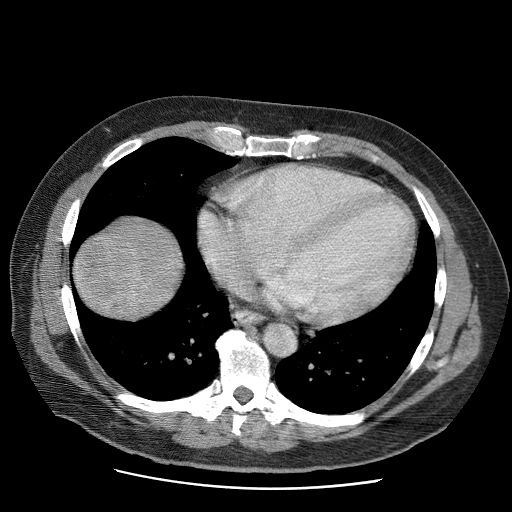
Contrast-enhanced abdominal CT (liver protocol), one axial slice. Position 65 of 81 along the scan axis. Reconstruction kernel STANDARD. Soft-tissue window (W 400 / L 40 HU). 2.5 mm slice thickness. 512 × 512 image matrix. Case-level facts recorded for this patient, not image findings: diagnosis: hepatocellular carcinoma (patient treated with transarterial chemoembolisation; whether this scan precedes or follows treatment is not stated here); TNM stage (as recorded): Stage-IIIA; Child-Pugh class: A; tumour differentiation: moderately differentiated; tumour nodularity: multinodular.
Outlined on this slice (semi-automatic segmentation, software-assisted and operator-edited):
- liver parenchyma outside the tumour (the mass and vessels are separate outlines, so this box may not span the whole liver): bounding box <72,216,182,318> (left, top, right, bottom; pixels)
- mass: <74,232,142,316>